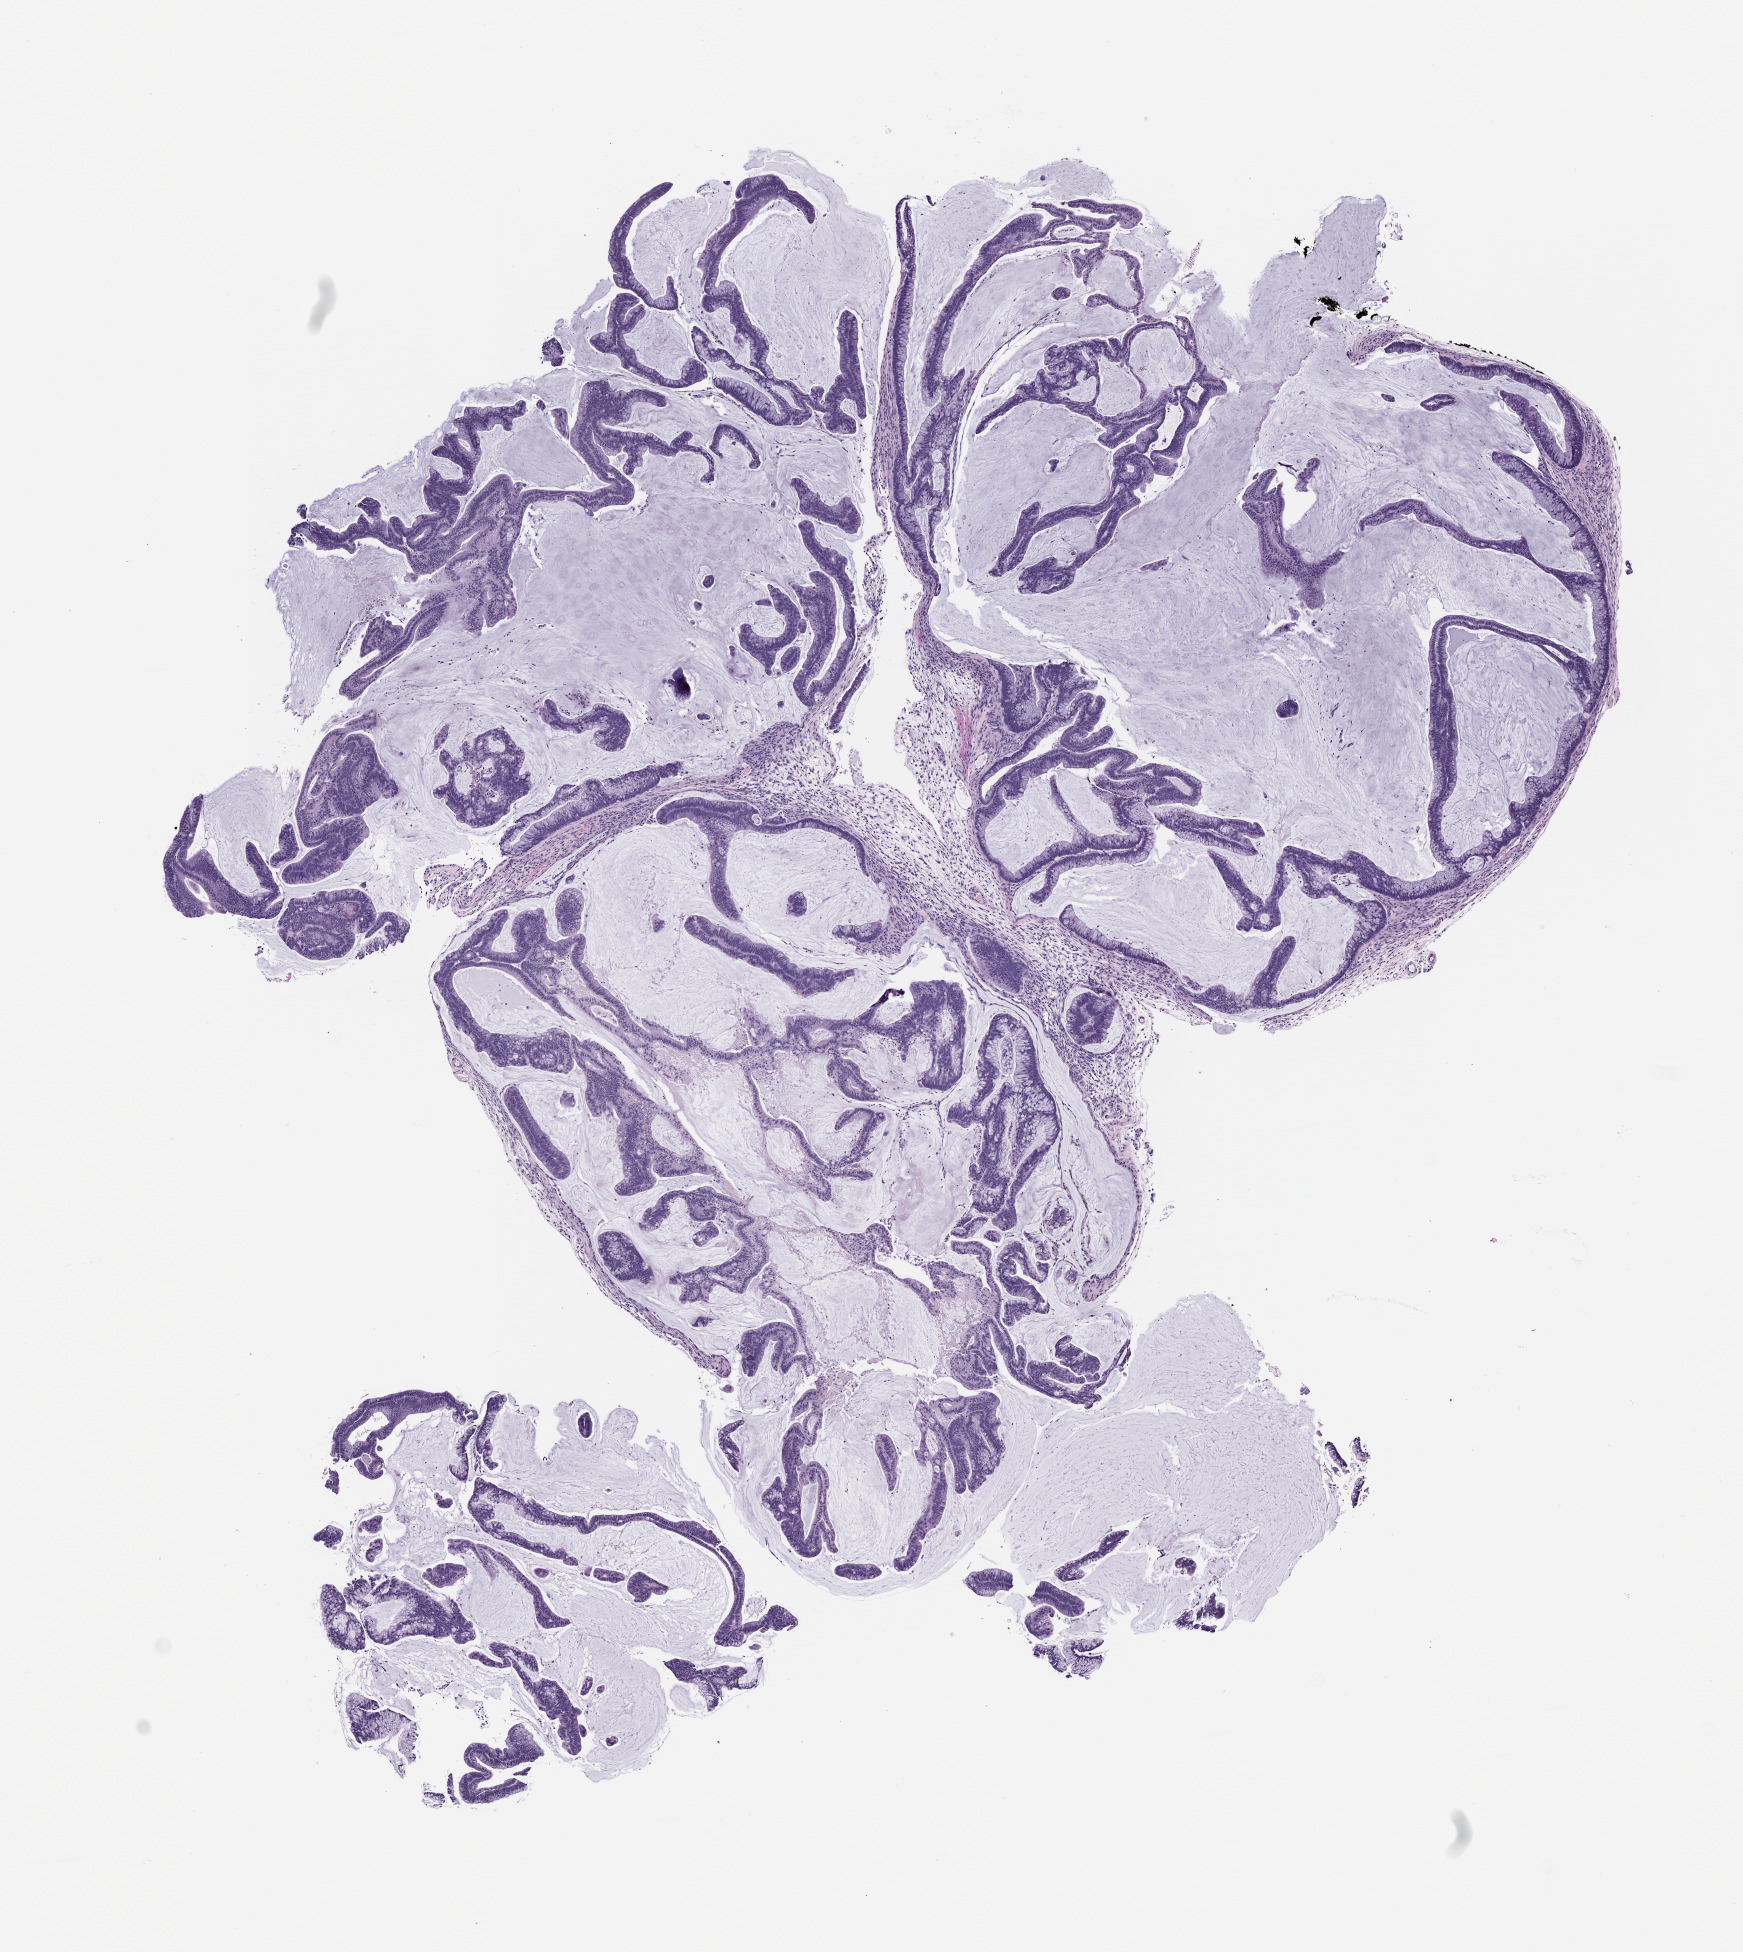
Whole-slide image, haematoxylin and eosin: patient-derived xenograft (human tumor grown in a mouse), passage 1 — low-resolution overview of the scanned area, about 7.0 x 7.9 mm. FFPE section. Originating tumor site category: colon.
Originating patient diagnosis: Colon Adenocarcinoma.